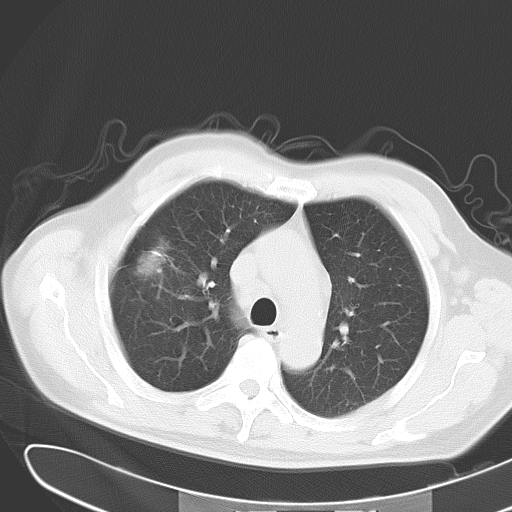
Chest CT, one axial slice; slice 22 of 31 in the series (ordered by position); reconstruction kernel B70f; 120 kVp; lung window (W 1500 / L -600 HU); 512 × 512 image matrix, field of view 364 × 364 mm. Patient: male, 59 years. Case-level facts recorded for this patient, not image findings: clinical TNM (as recorded): T2 N3 M0.
Outlined on this slice (bounding box drawn by a radiologist):
- lung tumour (recorded histology: adenocarcinoma): bounding box [x1, y1, x2, y2] px = [134, 236, 176, 279]